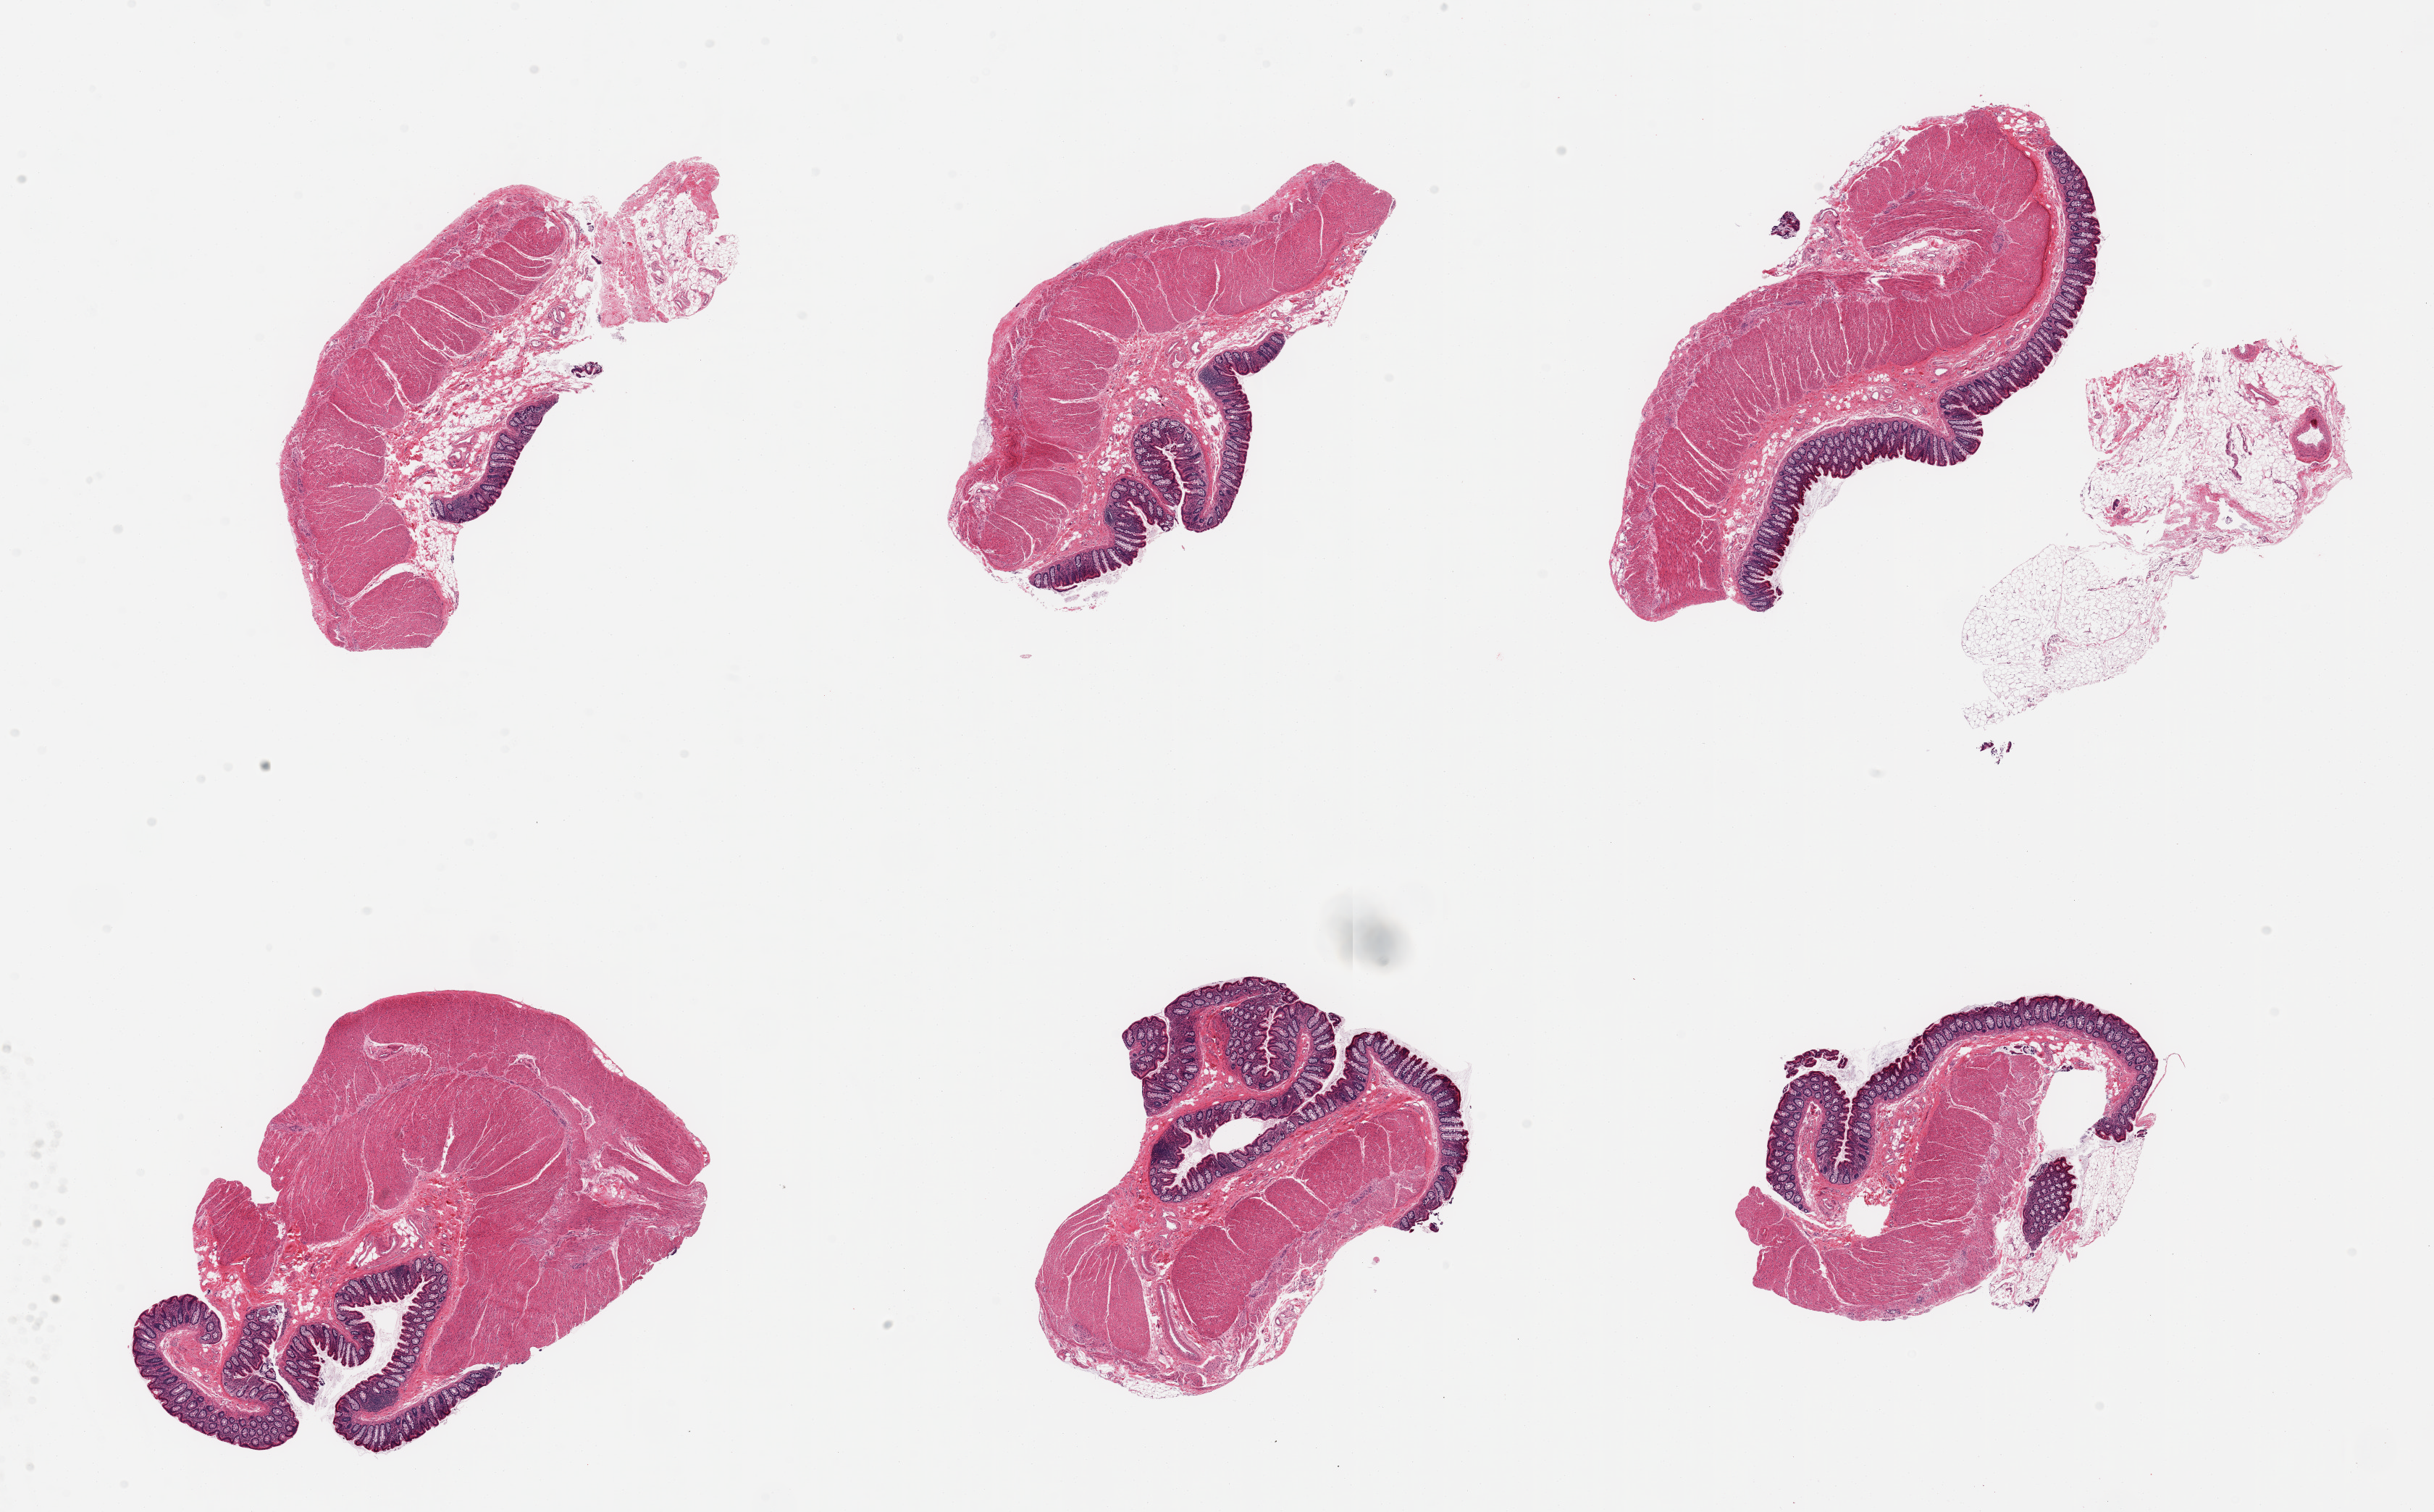
Whole-slide image, H&E stain — low-resolution overview of the scanned area, about 26.6 x 16.5 mm (slide scanned at 20x). PAXgene-fixed paraffin-embedded (PFPE) section. Target tissue: transverse colon. Tissue donor sample. Donor: male.
Pathologist's review note for this sample: 6 pieces, target mucosa well-preserved, ).35mm, ~10% total thickness.